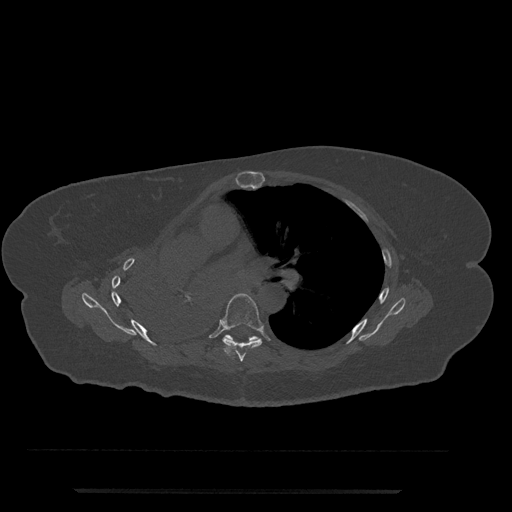
CT including the spine, one axial slice; bone window (W 1800 / L 400 HU); 0.5 mm slice thickness; 512 × 512 image matrix. Patient: female, 51 years. From the clinical record (not read from this slice): primary cancer: neuro.
Annotated regions visible in this slice (semi-automatically segmented with operator editing):
- T6 vertebra: bounding box [x1, y1, x2, y2] px = [221, 293, 263, 362]
- T7 vertebra: [225, 335, 260, 341]